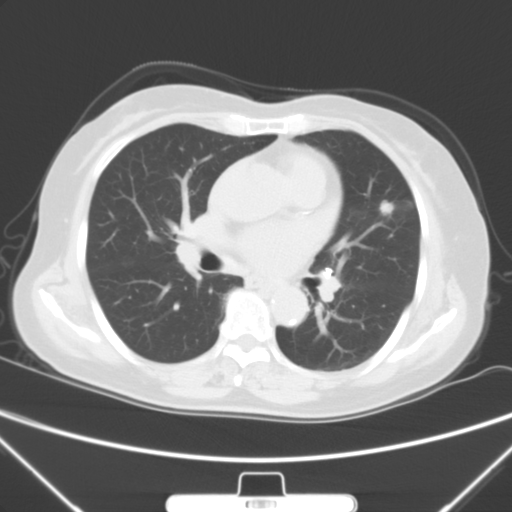
Chest CT, one axial slice; position 30 of 60 along the scan axis; lung window (W 1500 / L -600 HU); 512 × 512 image matrix. Patient: female, 70 years. From the clinical record (not read from this slice): clinical TNM (as recorded): T1b N0 M0; histopathological grade: G2.
Structures marked on this image (bounding box drawn by a radiologist):
- lung tumour (recorded histology: adenocarcinoma): bounding box [x1, y1, x2, y2] px = [372, 193, 401, 226]